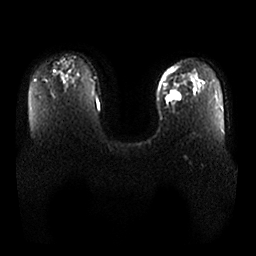
Breast MRI, one axial slice. Slice 18 of 25 in the series (ordered by position). Diffusion-weighted series; image 2 of 4 stored at this slice position (different b-values; order by instance number). 1.5 T. 256 × 256 image matrix. Female patient.
Annotated regions visible in this slice (manually delineated by an expert):
- tumour on diffusion-weighted imaging: box from (x=164, y=89) to (x=182, y=106) px